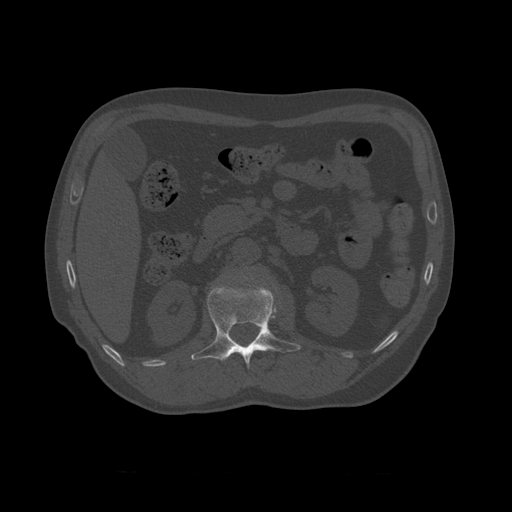
CT including the spine, one axial slice. Position 353 of 450 along the scan axis. Reconstruction kernel STANDARD. Bone window (W 1800 / L 400 HU). 1.25 mm slice thickness. 512 × 512 image matrix. Patient age 75 years. From the clinical record (not read from this slice): primary cancer: prostate.
Outlined on this slice (semi-automatic segmentation, software-assisted and operator-edited):
- L1 vertebra: bounding box <191,283,301,369> (left, top, right, bottom; pixels)
- T11 vertebra: <225,356,227,359>